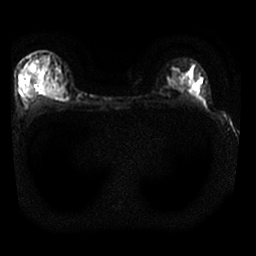
Breast MRI, one axial slice. Slice 19 of 25 in the series (ordered by position). Diffusion-weighted series; image 2 of 4 stored at this slice position (different b-values; order by instance number). 1.5 T. 4 mm slice thickness. 256 × 256 image matrix, field of view 310 × 310 mm. Female patient.
Annotated regions visible in this slice (manually delineated by an expert):
- tumour on diffusion-weighted imaging: bounding box <38,80,61,94> (left, top, right, bottom; pixels)